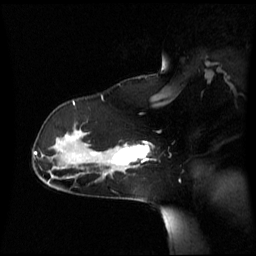
Breast MRI (dynamic contrast-enhanced), one sagittal slice. Position 42 of 60 along the scan axis. Dynamic contrast-enhanced series, image 2 of 3 at this slice position (ordered by acquisition). 1.5 T. TE 4.2 ms, TR 8.4 ms. 256 × 256 image matrix. Female patient, age 39 years. From the clinical record (not read from this slice): setting: breast cancer imaged before/during neoadjuvant chemotherapy; receptor status: triple-negative.
Annotated regions visible in this slice (semi-automatic segmentation, software-assisted and operator-edited):
- analysis volume of interest (the breast-tissue region the enhancement analysis was run in; not a lesion): bounding box [x1, y1, x2, y2] px = [101, 143, 149, 173]
- tumour enhancement mask (voxels above the 70 % enhancement threshold inside the analysis volume of interest): [114, 145, 149, 165]